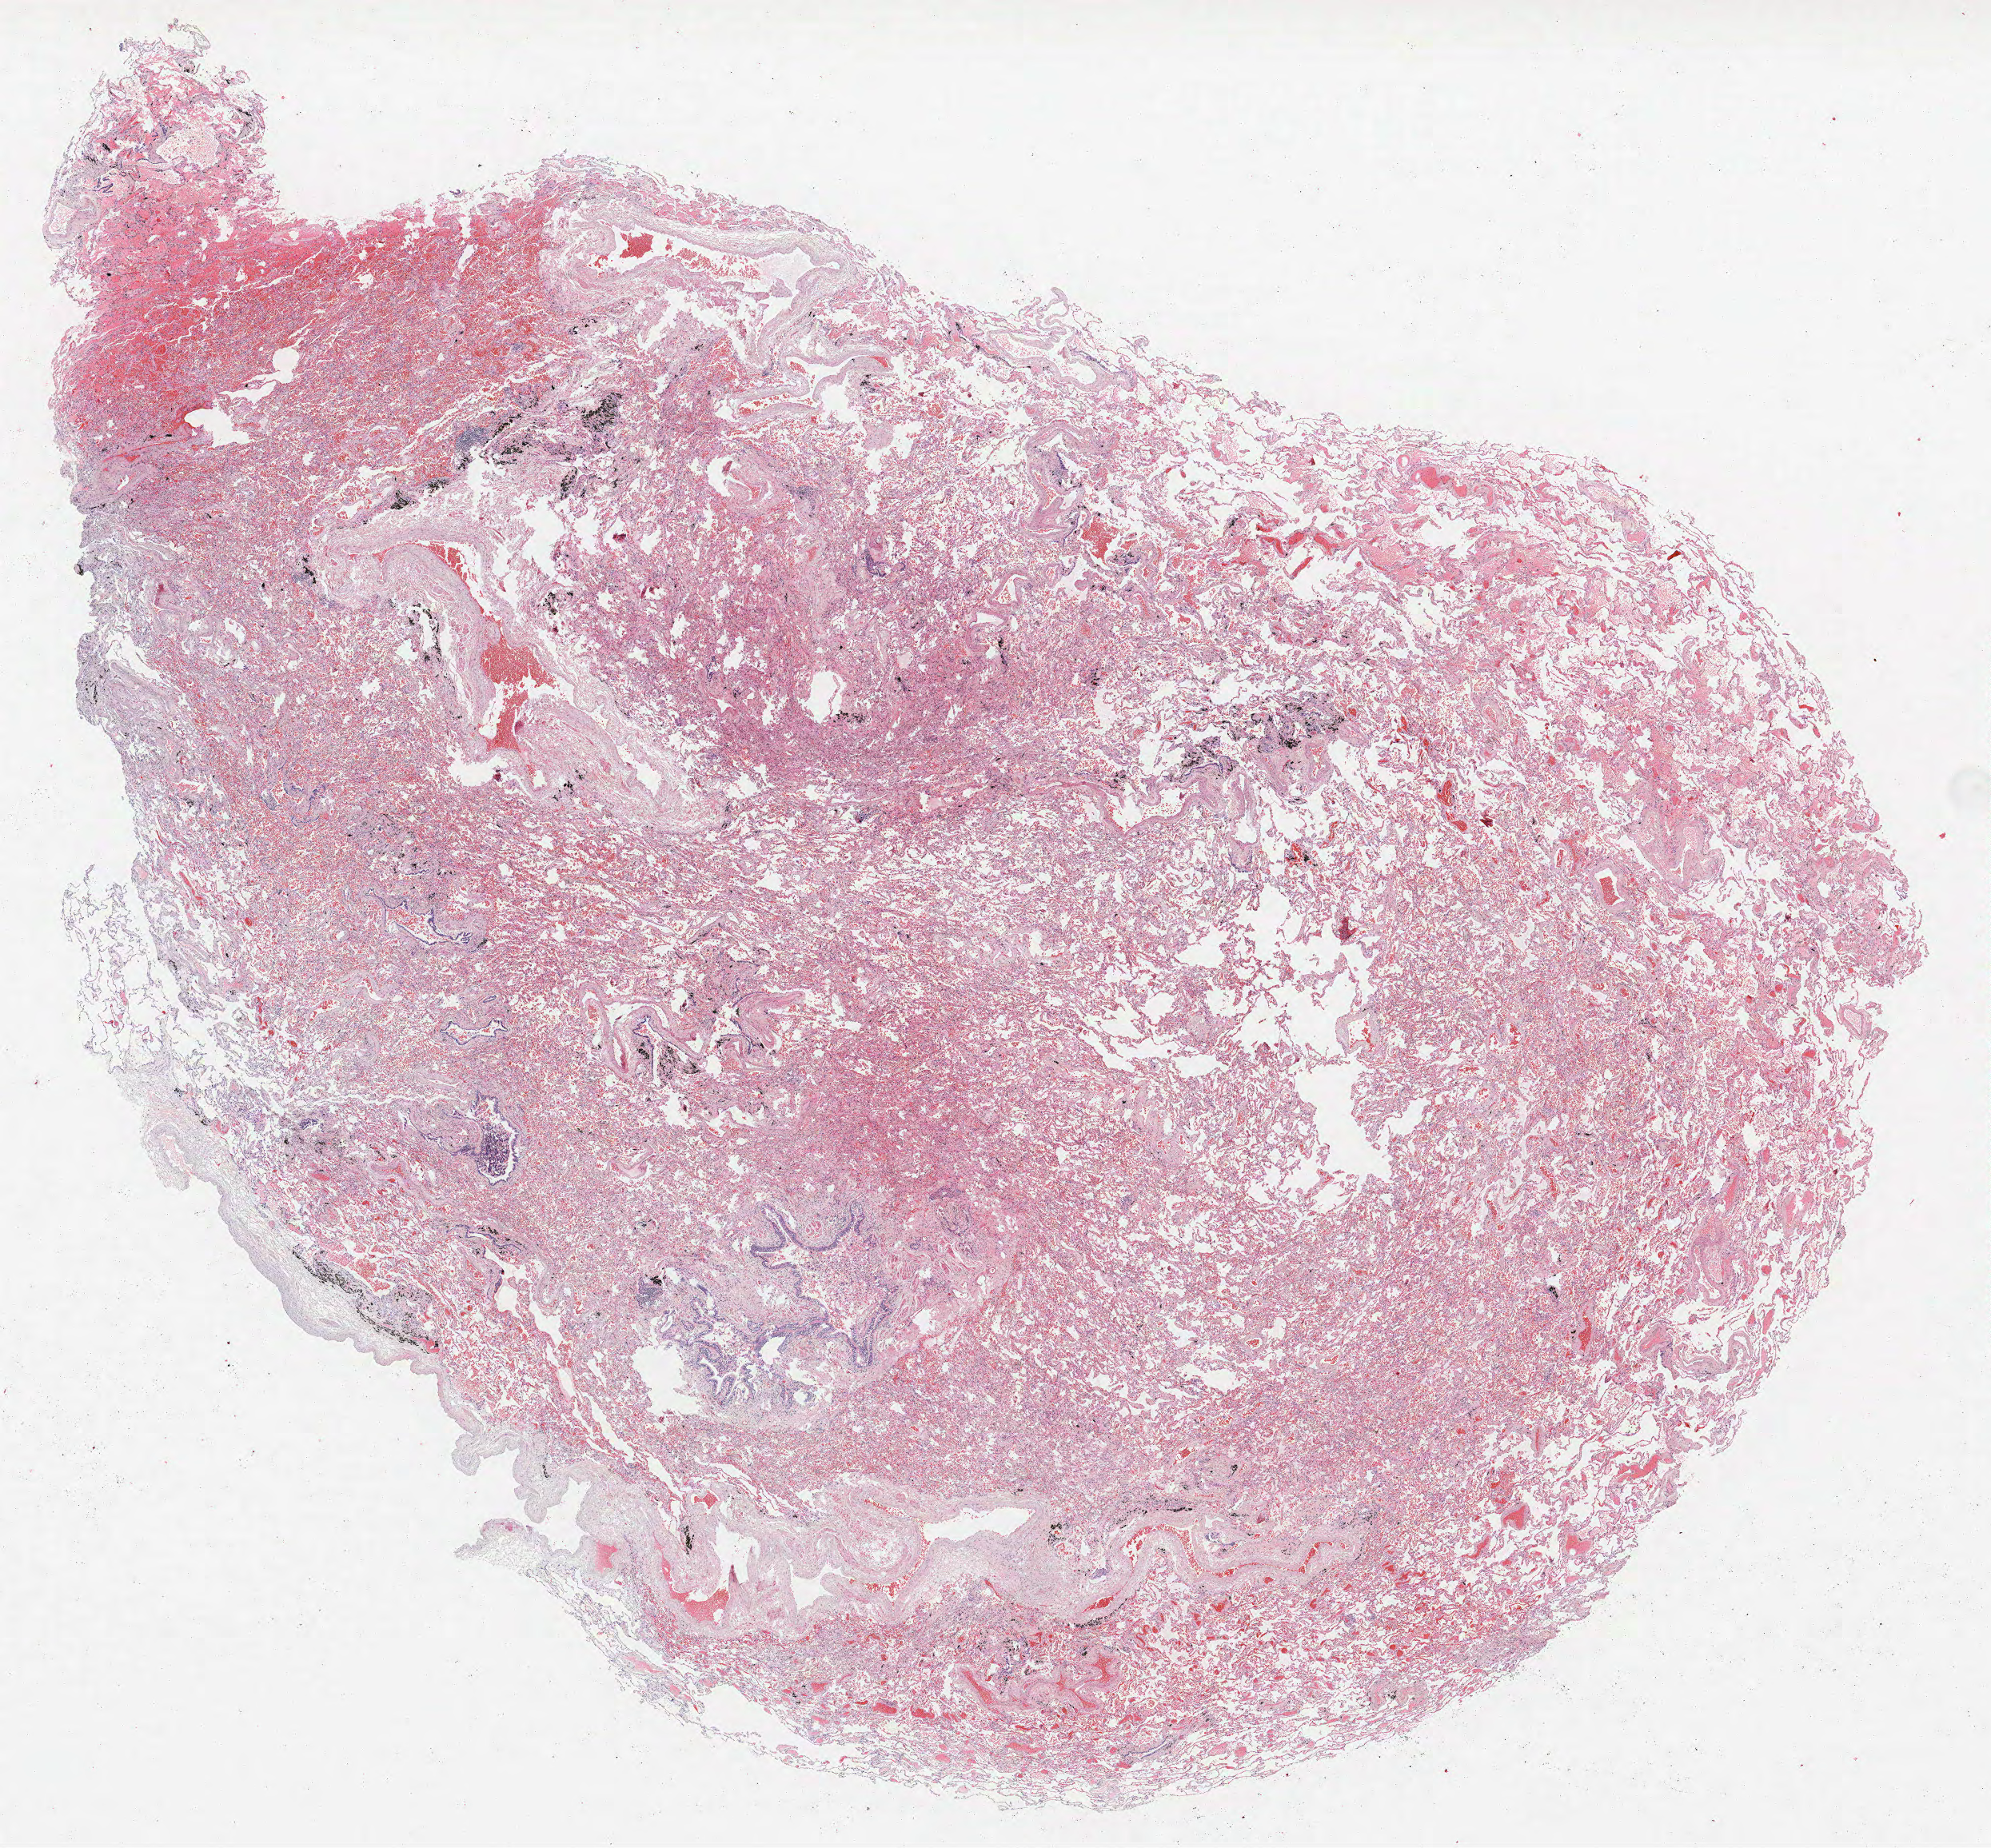
H&E whole-slide image — whole scanned area (about 19.9 x 18.5 mm, acquisition: 40x scan) shown as a low-resolution overview. FFPE section. Lung. Male patient, aged 73 at enrolment. Former smoker at enrolment.
* primary tumour location (clinical record): right lower lobe
* stage (AJCC 6th edition): IA
* ICD-O-3 topography: lower lobe of lung (C34.3)
* tumour size (pathology): 30 mm
* participant's lung-cancer diagnosis: Non-small cell carcinoma